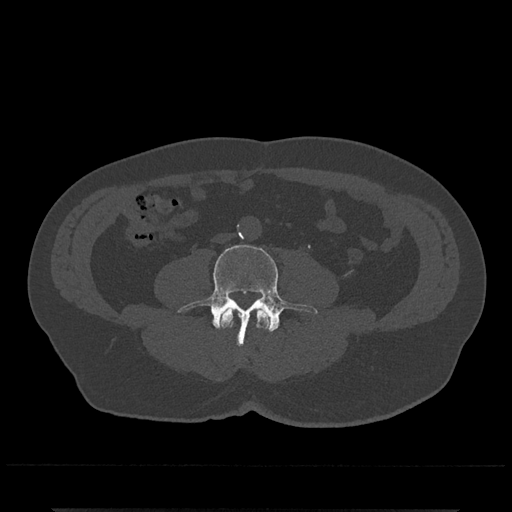
CT including the spine, one axial slice. Position 166 of 797 along the scan axis. 120 kVp. Bone window (W 1800 / L 400 HU). 0.5 mm slice thickness. 512 × 512 image matrix. Patient: male, 67 years. Case-level facts recorded for this patient, not image findings: primary cancer: prostate.
Outlined on this slice (semi-automatically segmented with operator editing):
- L3 vertebra: bounding box <219,308,271,331> (left, top, right, bottom; pixels)
- L4 vertebra: <178,244,317,346>